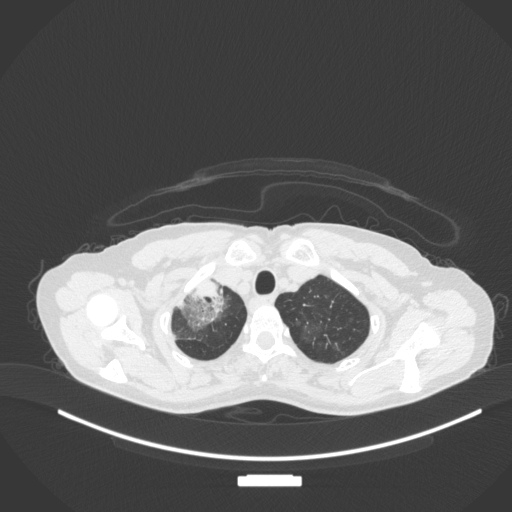
Chest CT, one axial slice. Slice 288 of 311 in the series (ordered by position). Reconstruction kernel B31f. Lung window (W 1500 / L -600 HU). 1 mm slice thickness. 512 × 512 image matrix. Patient: female, 59 years. From the clinical record (not read from this slice): clinical TNM (as recorded): T3 N0 M0.
Outlined on this slice (rectangle marked by the reading radiologist):
- lung tumour (recorded histology: adenocarcinoma): bounding box (x1, y1, x2, y2) in pixels: (166, 268, 231, 334)